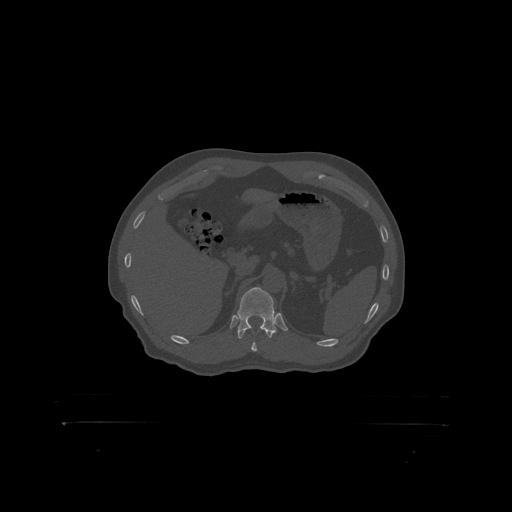
CT including the spine, one axial slice; slice 360 of 399 in the series (ordered by position); reconstruction kernel STANDARD; 120 kVp; bone window (W 1800 / L 400 HU); 1.25 mm slice thickness; 512 × 512 image matrix, field of view 650 × 650 mm. Patient: male, 46 years. Case-level facts recorded for this patient, not image findings: primary cancer: skin.
Structures marked on this image (semi-automatically segmented with operator editing):
- T12 vertebra: bounding box <238,288,281,319> (left, top, right, bottom; pixels)